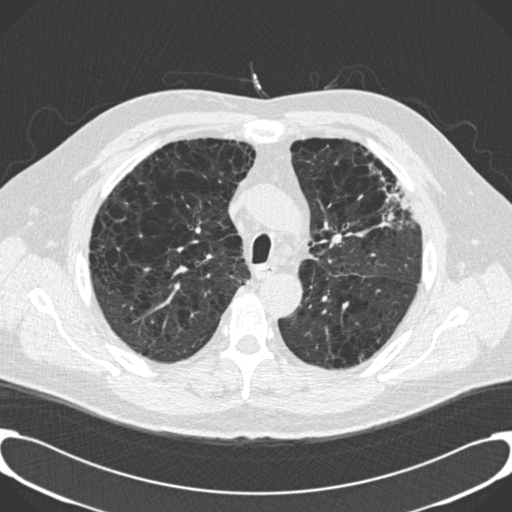
Low-dose screening chest CT, one axial slice; position 143 of 189 along the scan axis; lung window (W 1500 / L -600 HU); 512 × 512 image matrix, field of view 380 × 380 mm.
Outlined on this slice (outlined manually by an expert reader):
- lesion 1 (tumor, upper lobe of left lung): bounding box <385,179,416,221> (left, top, right, bottom; pixels)